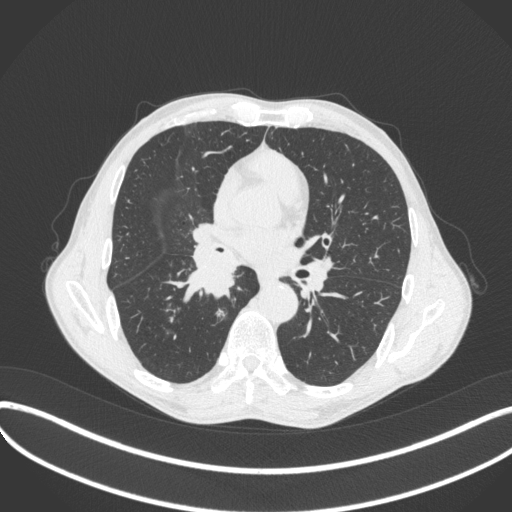
Chest CT, one axial slice; position 225 of 481 along the scan axis; reconstruction kernel B31f; lung window (W 1500 / L -600 HU); 1 mm slice thickness; 512 × 512 image matrix. Patient: male, 65 years. From the clinical record (not read from this slice): clinical TNM (as recorded): T2a N0 M0.
Annotated regions visible in this slice (rectangle marked by the reading radiologist):
- lung tumour (recorded histology: squamous cell carcinoma): bounding box (x1, y1, x2, y2) in pixels: (186, 227, 247, 306)